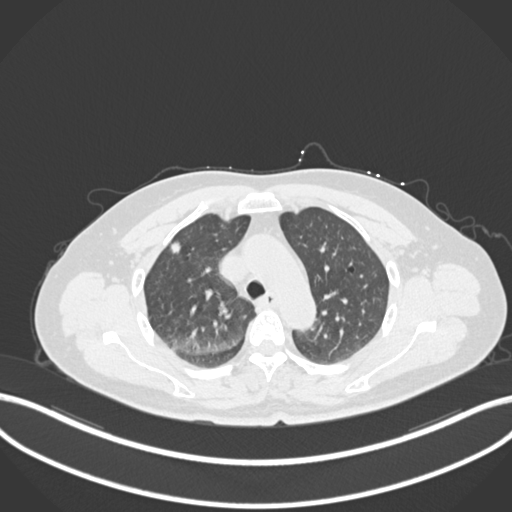
Chest CT, one axial slice; slice 168 of 223 in the series (ordered by position); reconstruction kernel B30f; lung window (W 1500 / L -600 HU); 1 mm slice thickness; 512 × 512 image matrix, field of view 400 × 400 mm. Patient: female, 56 years. From the clinical record (not read from this slice): clinical TNM (as recorded): T1c N0 M0.
Annotated regions visible in this slice (rectangle marked by the reading radiologist):
- lung tumour (recorded histology: adenocarcinoma): bounding box <165,236,189,257> (left, top, right, bottom; pixels)